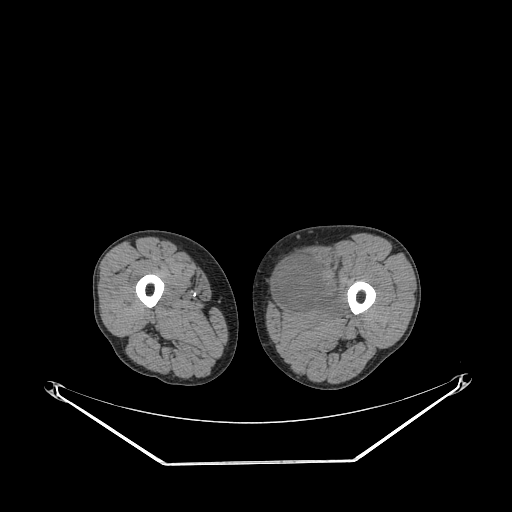
CT of an extremity soft-tissue mass (from a PET/CT study), one axial slice. Slice 231 of 267 in the series (ordered by position). Reconstruction kernel STANDARD. 140 kVp. Soft-tissue window (W 400 / L 40 HU). 3.75 mm slice thickness. 512 × 512 image matrix, field of view 500 × 500 mm. Male patient. From the clinical record (not read from this slice): histological type: pleiomorphic liposarcoma; grade: high; site of the primary tumour: left thigh.
Structures marked on this image (expert contour drawn on MRI and transferred to this co-registered scan by the dataset authors):
- gross tumour volume including surrounding oedema: bounding box [x1, y1, x2, y2] px = [276, 253, 344, 318]
- gross tumour volume (mass): [276, 254, 325, 309]